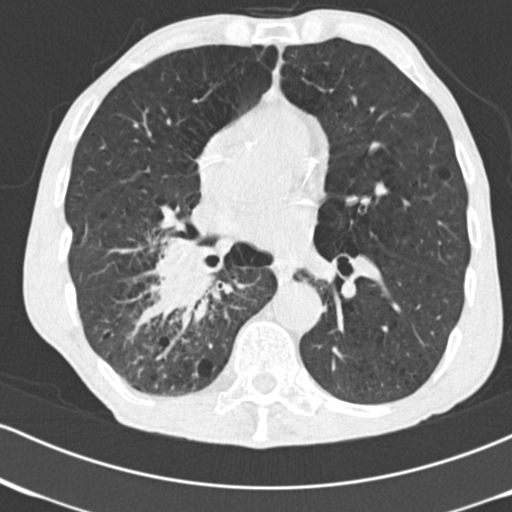
Axial slice from a low-dose chest CT screening exam; second annual screen; lung window (W 1500 / L -600 HU); standard (soft-tissue) reconstruction kernel (B30f); 120 kVp; slice 103 of 182 in the series; 512 × 512 image matrix, field of view 316 × 316 mm. Male participant, aged 64 years at enrolment. Current smoker at enrolment.
Expert reader's lesion annotation, bounding box (x1, y1, x2, y2) in pixels: (126, 226, 242, 336). The exam's reader record, not a measurement of the box and not confirmed to be the same lesion: non-calcified nodule or mass ≥4 mm, 52 × 37 mm, spiculated (stellate) margins, soft tissue attenuation, pre-existing on the prior screen: no. Participant outcome: lung cancer diagnosed 28 days after this screen — adenocarcinoma, NOS, right lower lobe, stage IV (AJCC 6th edition), 60 mm at pathology.